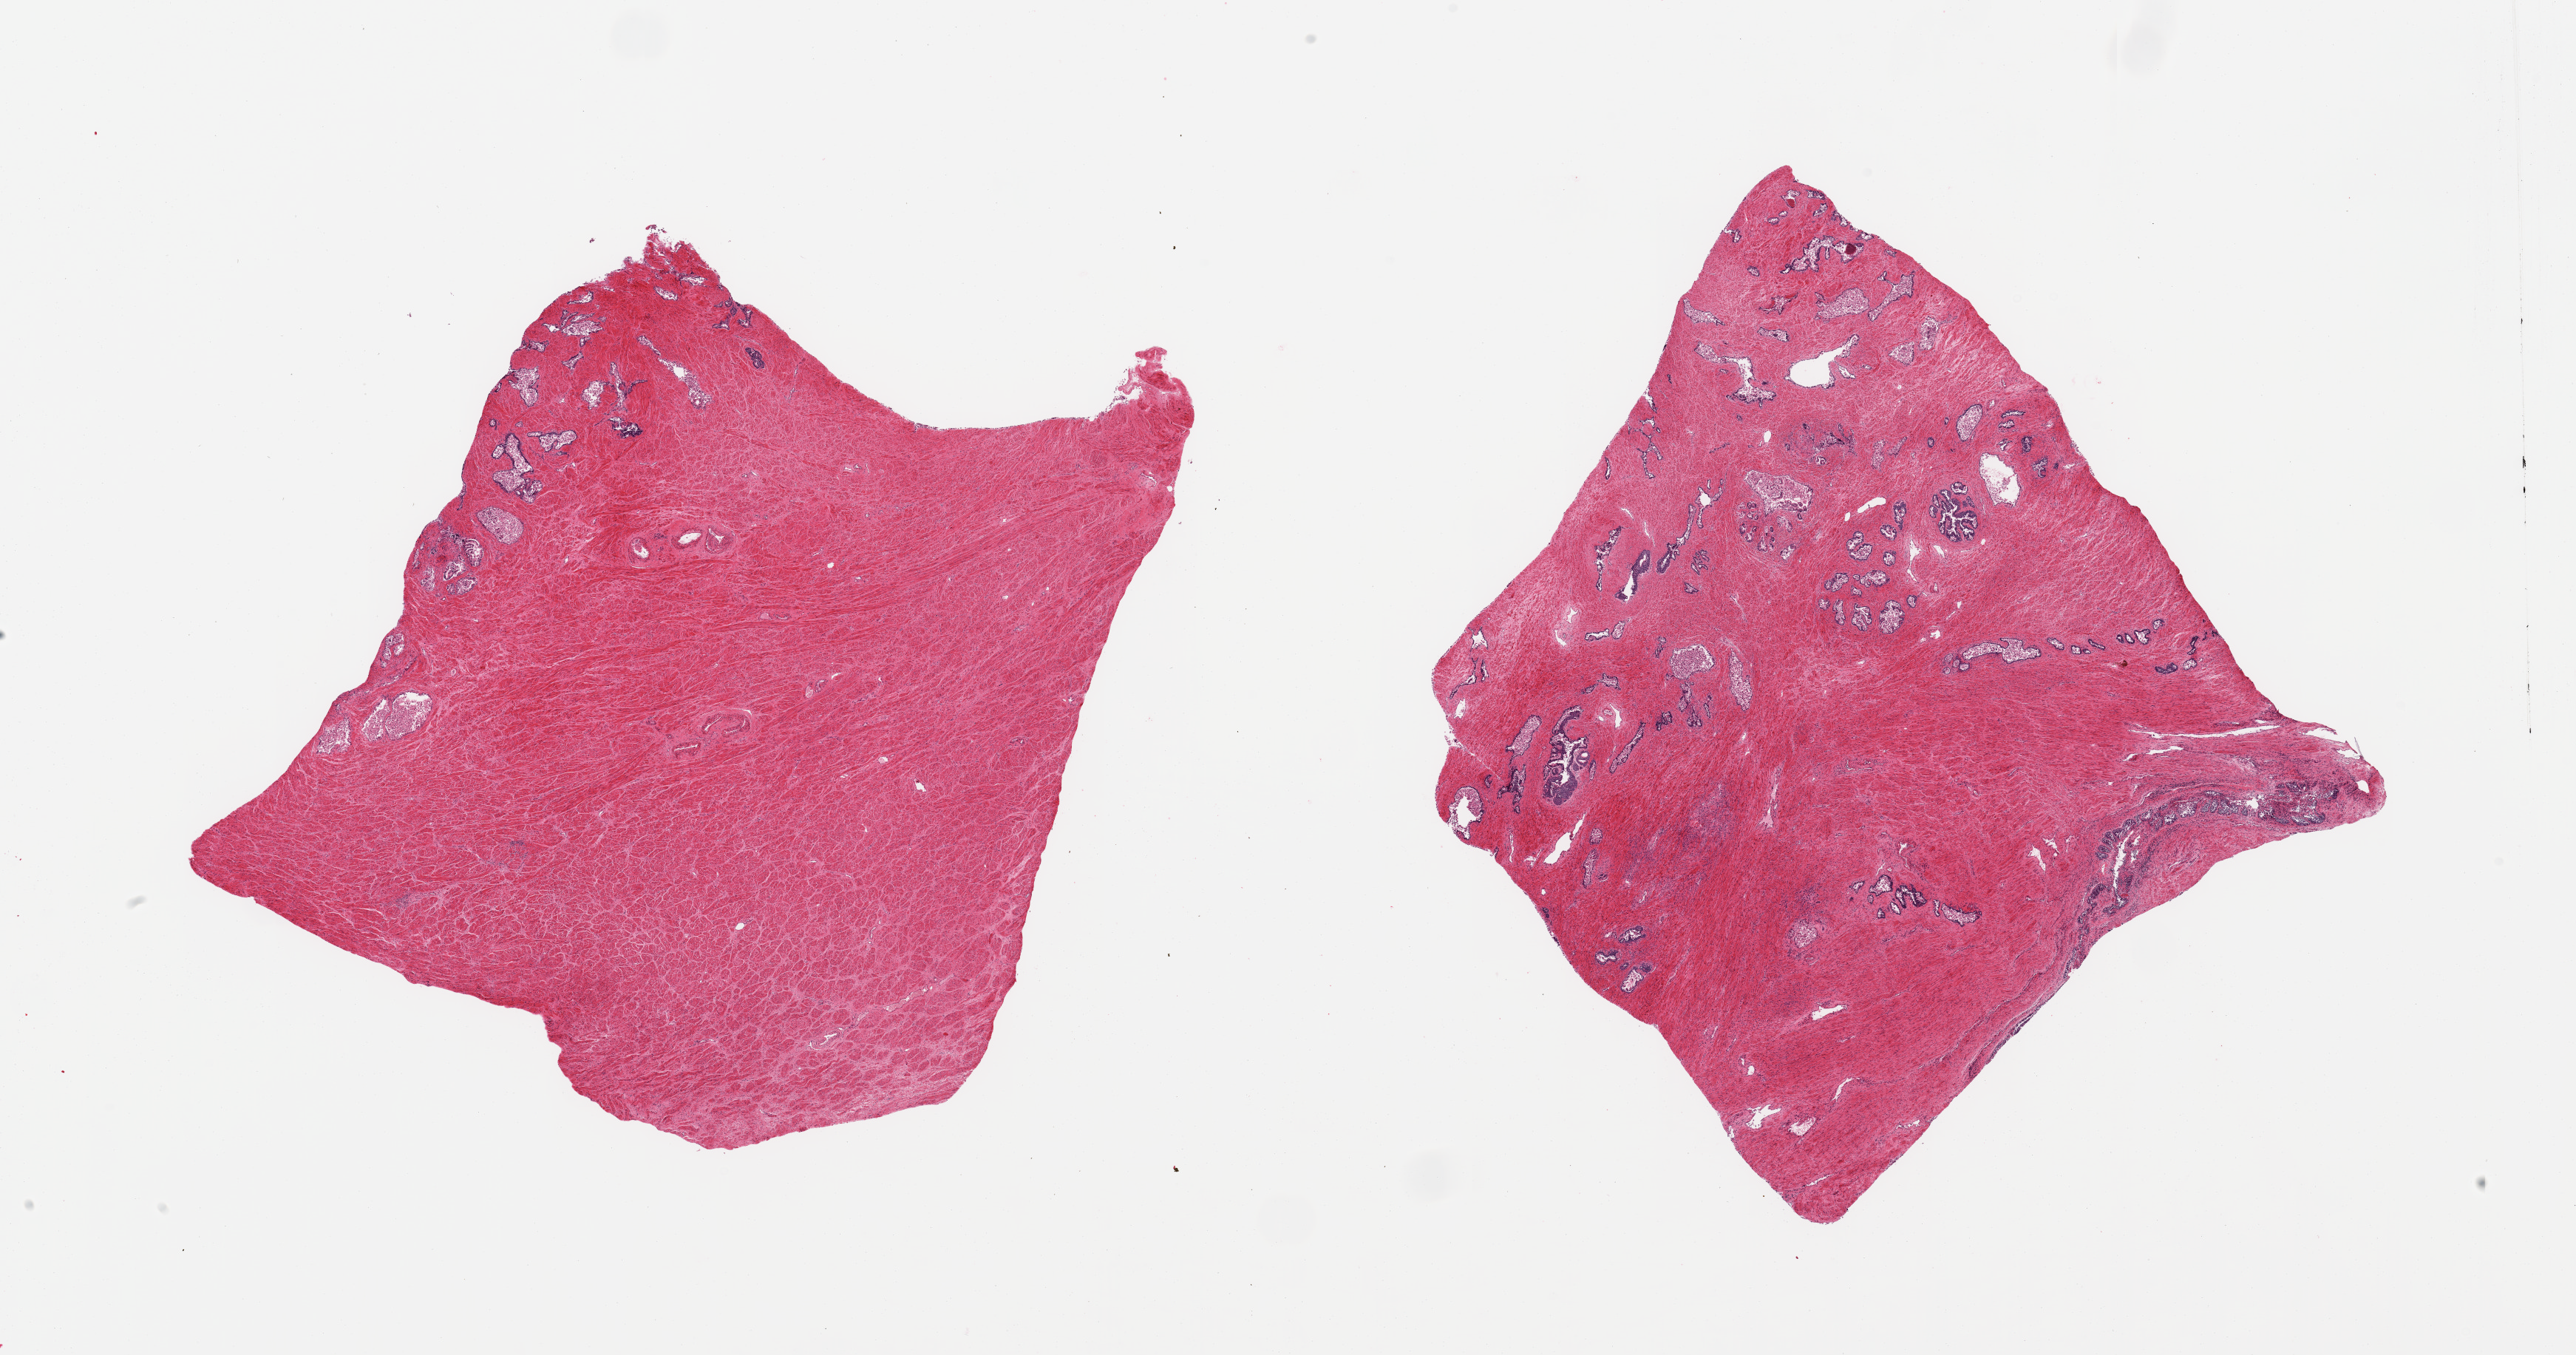
Haematoxylin and eosin whole-slide image, a low-resolution overview of the entire scanned area, about 27.6 x 14.5 mm. PAXgene-fixed paraffin-embedded (PFPE) section. Target tissue: prostate. Donor tissue sample. Donor sex: male.
Reviewer comment on this tissue sample: 2 pieces, mainly stroma; glandular elements variably preserved, some with urothelial metaplasia.